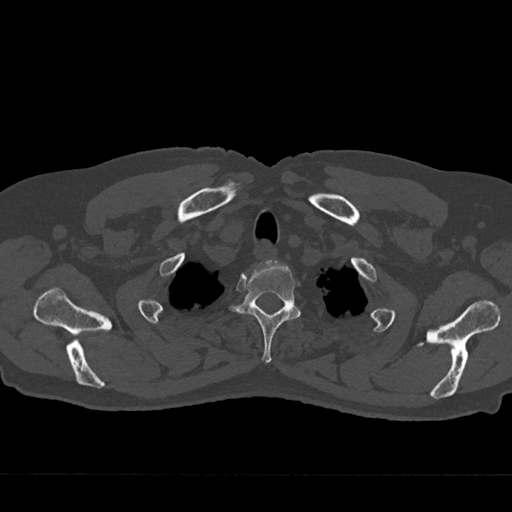
CT including the spine, one axial slice; position 614 of 797 along the scan axis; bone window (W 1800 / L 400 HU); 0.5 mm slice thickness; 512 × 512 image matrix, field of view 377 × 377 mm. Patient: male, 75 years. From the clinical record (not read from this slice): primary cancer: renal.
Annotated regions visible in this slice (semi-automatic segmentation, software-assisted and operator-edited):
- T2 vertebra: bounding box (x1, y1, x2, y2) in pixels: (230, 260, 301, 363)